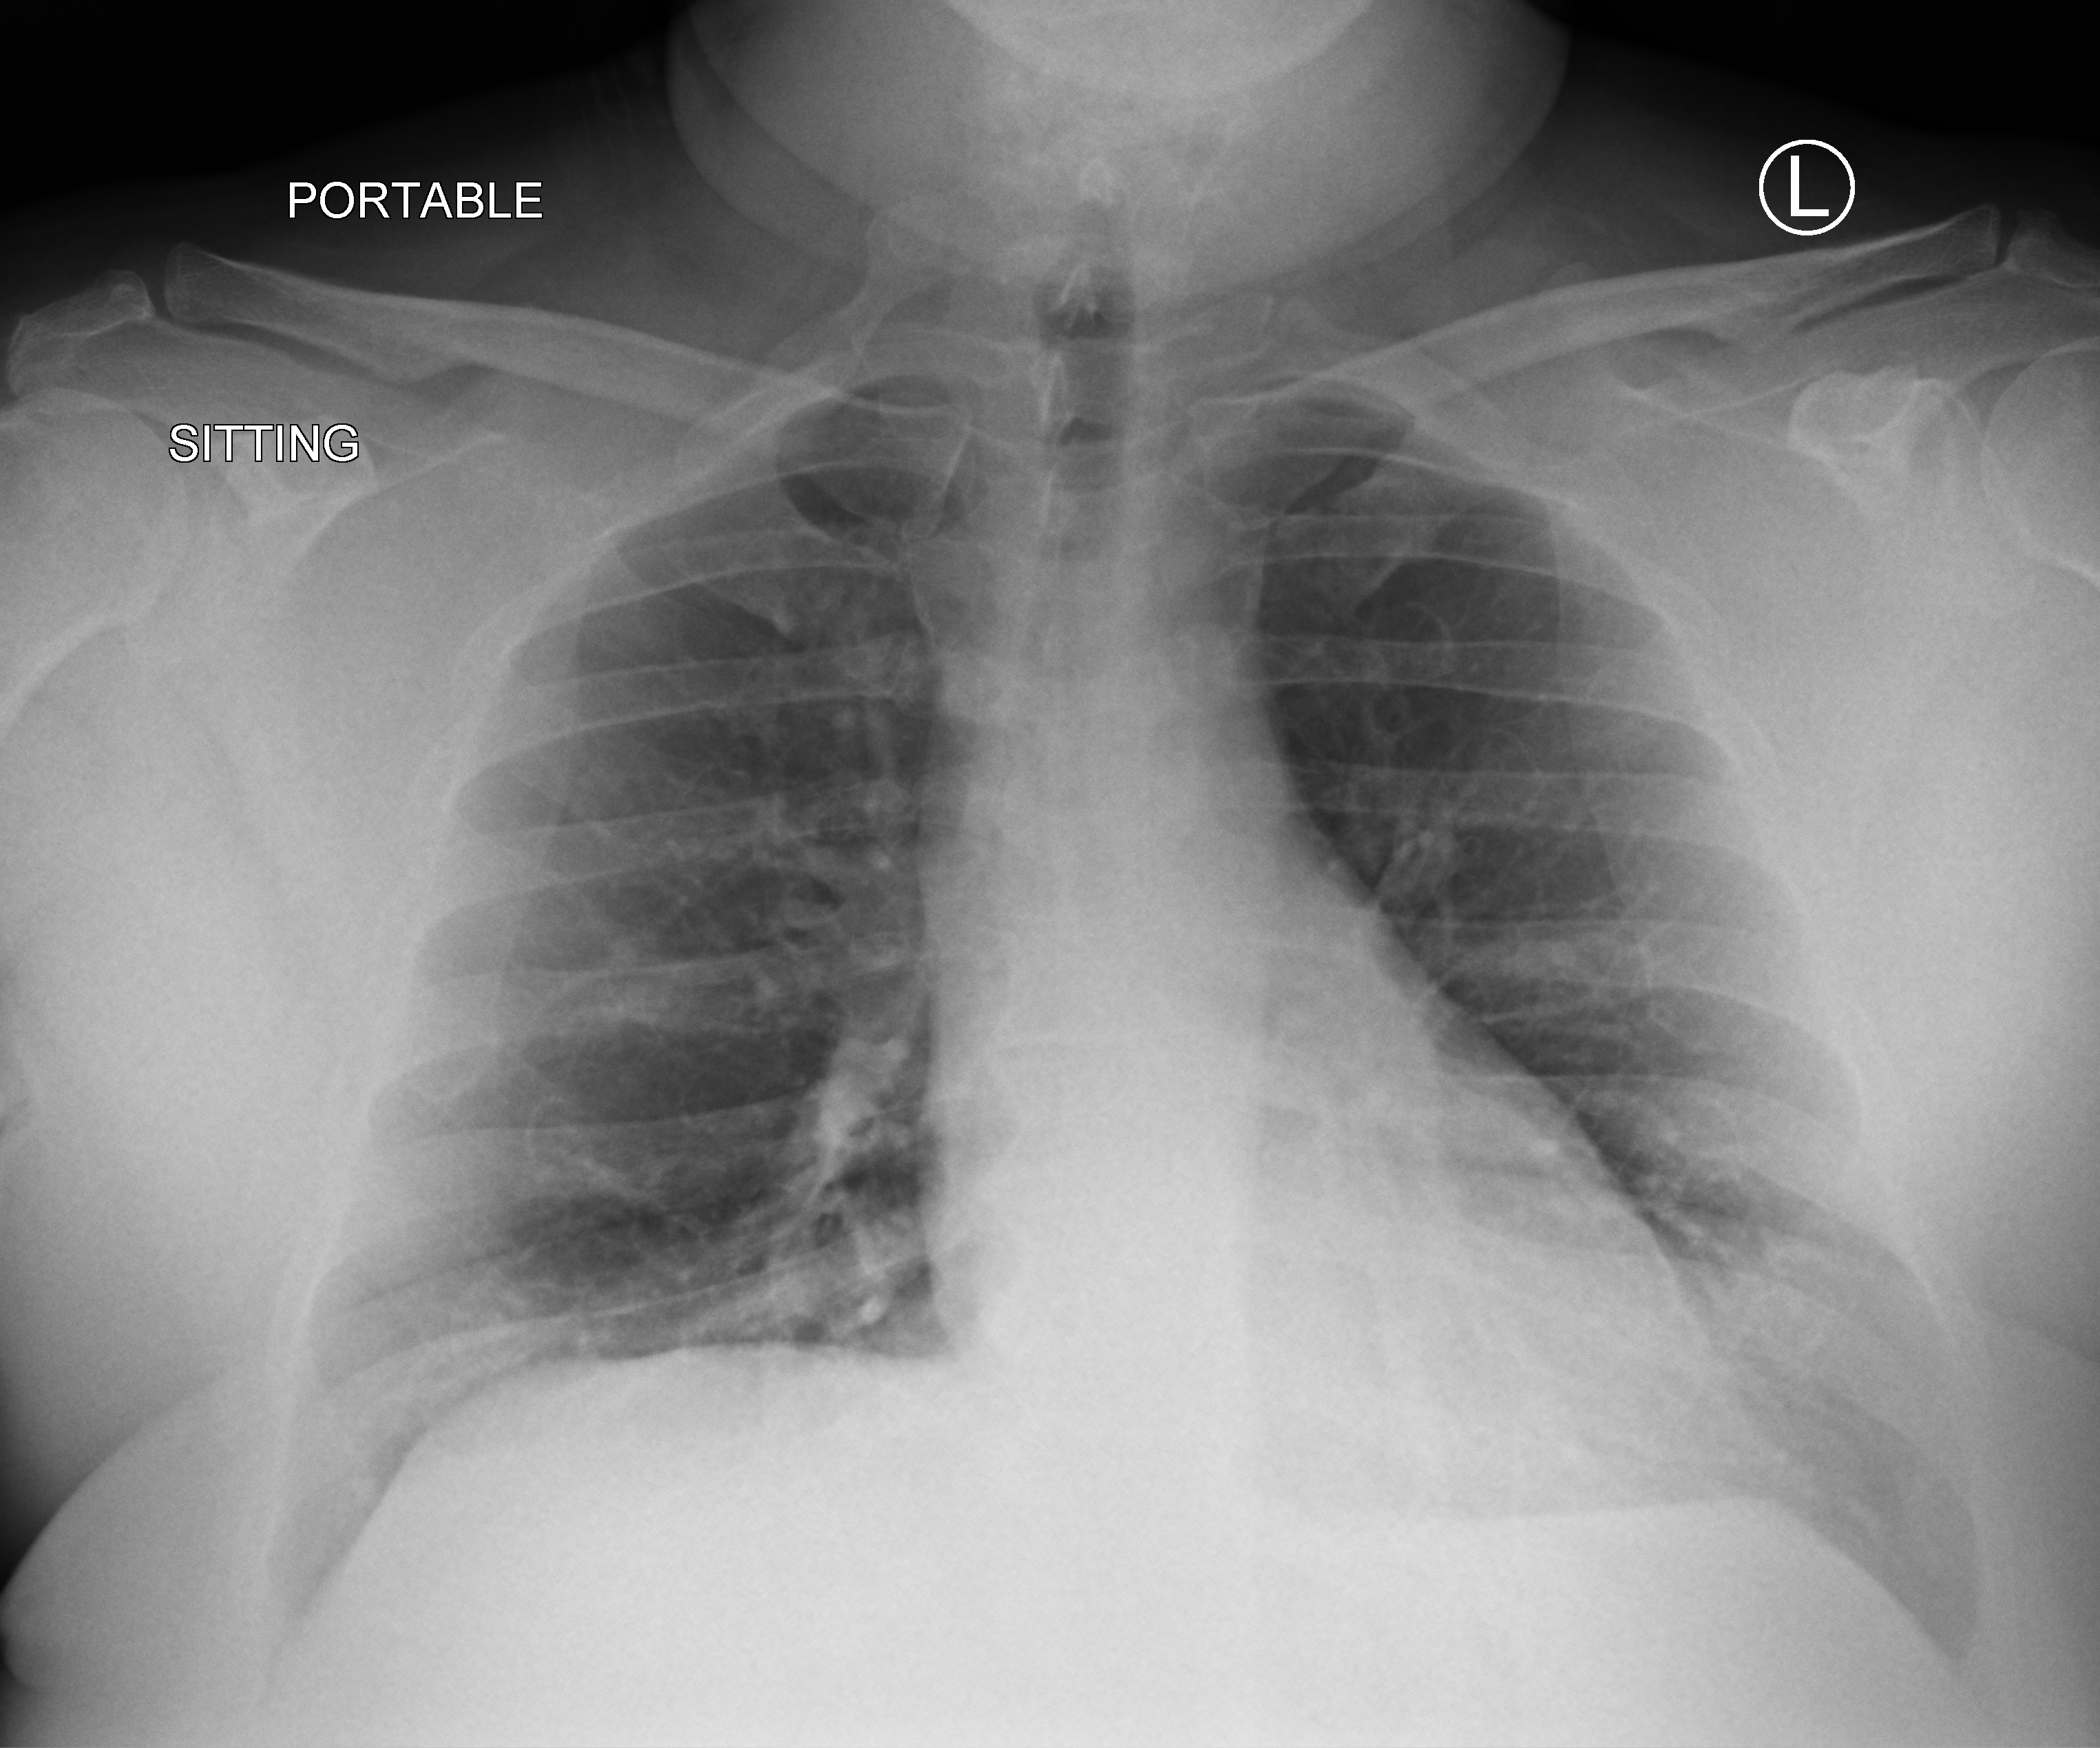
Chest X-ray (portable), anteroposterior (AP) projection. Male patient hospitalised with COVID-19, age 18–59 years.
Admission-level facts for this patient (not findings on this image; timing relative to this image not recorded): mechanically ventilated during this hospital stay: no; admitted to intensive care during this hospital stay: no.